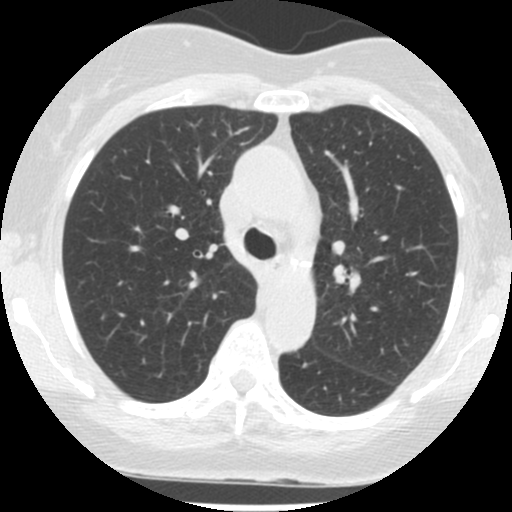
Chest CT (low-dose screening protocol), one axial image. Second annual screen. Lung window (W 1500 / L -600 HU). 2.5 mm slice thickness. Standard (soft-tissue) reconstruction kernel (STANDARD). 120 kVp. Slice 31 of 99 in the series. Female, age 62 years at enrolment. Former smoker at enrolment.
Expert reader's lesion annotation, box from (x=110, y=208) to (x=164, y=252) px. Screening reader's record for this exam (one nodule recorded; not confirmed to be the boxed lesion): non-calcified nodule or mass ≥4 mm, right upper lobe, 10 × 6 mm, spiculated (stellate) margins, soft tissue attenuation, pre-existing on the prior screen: yes; interval growth: yes. Official screen result: positive, other. Lung cancer was diagnosed 515 days after this screen: adenocarcinoma, NOS, right upper lobe, well differentiated (G1), stage IA (AJCC 6th edition), 7 mm at pathology.